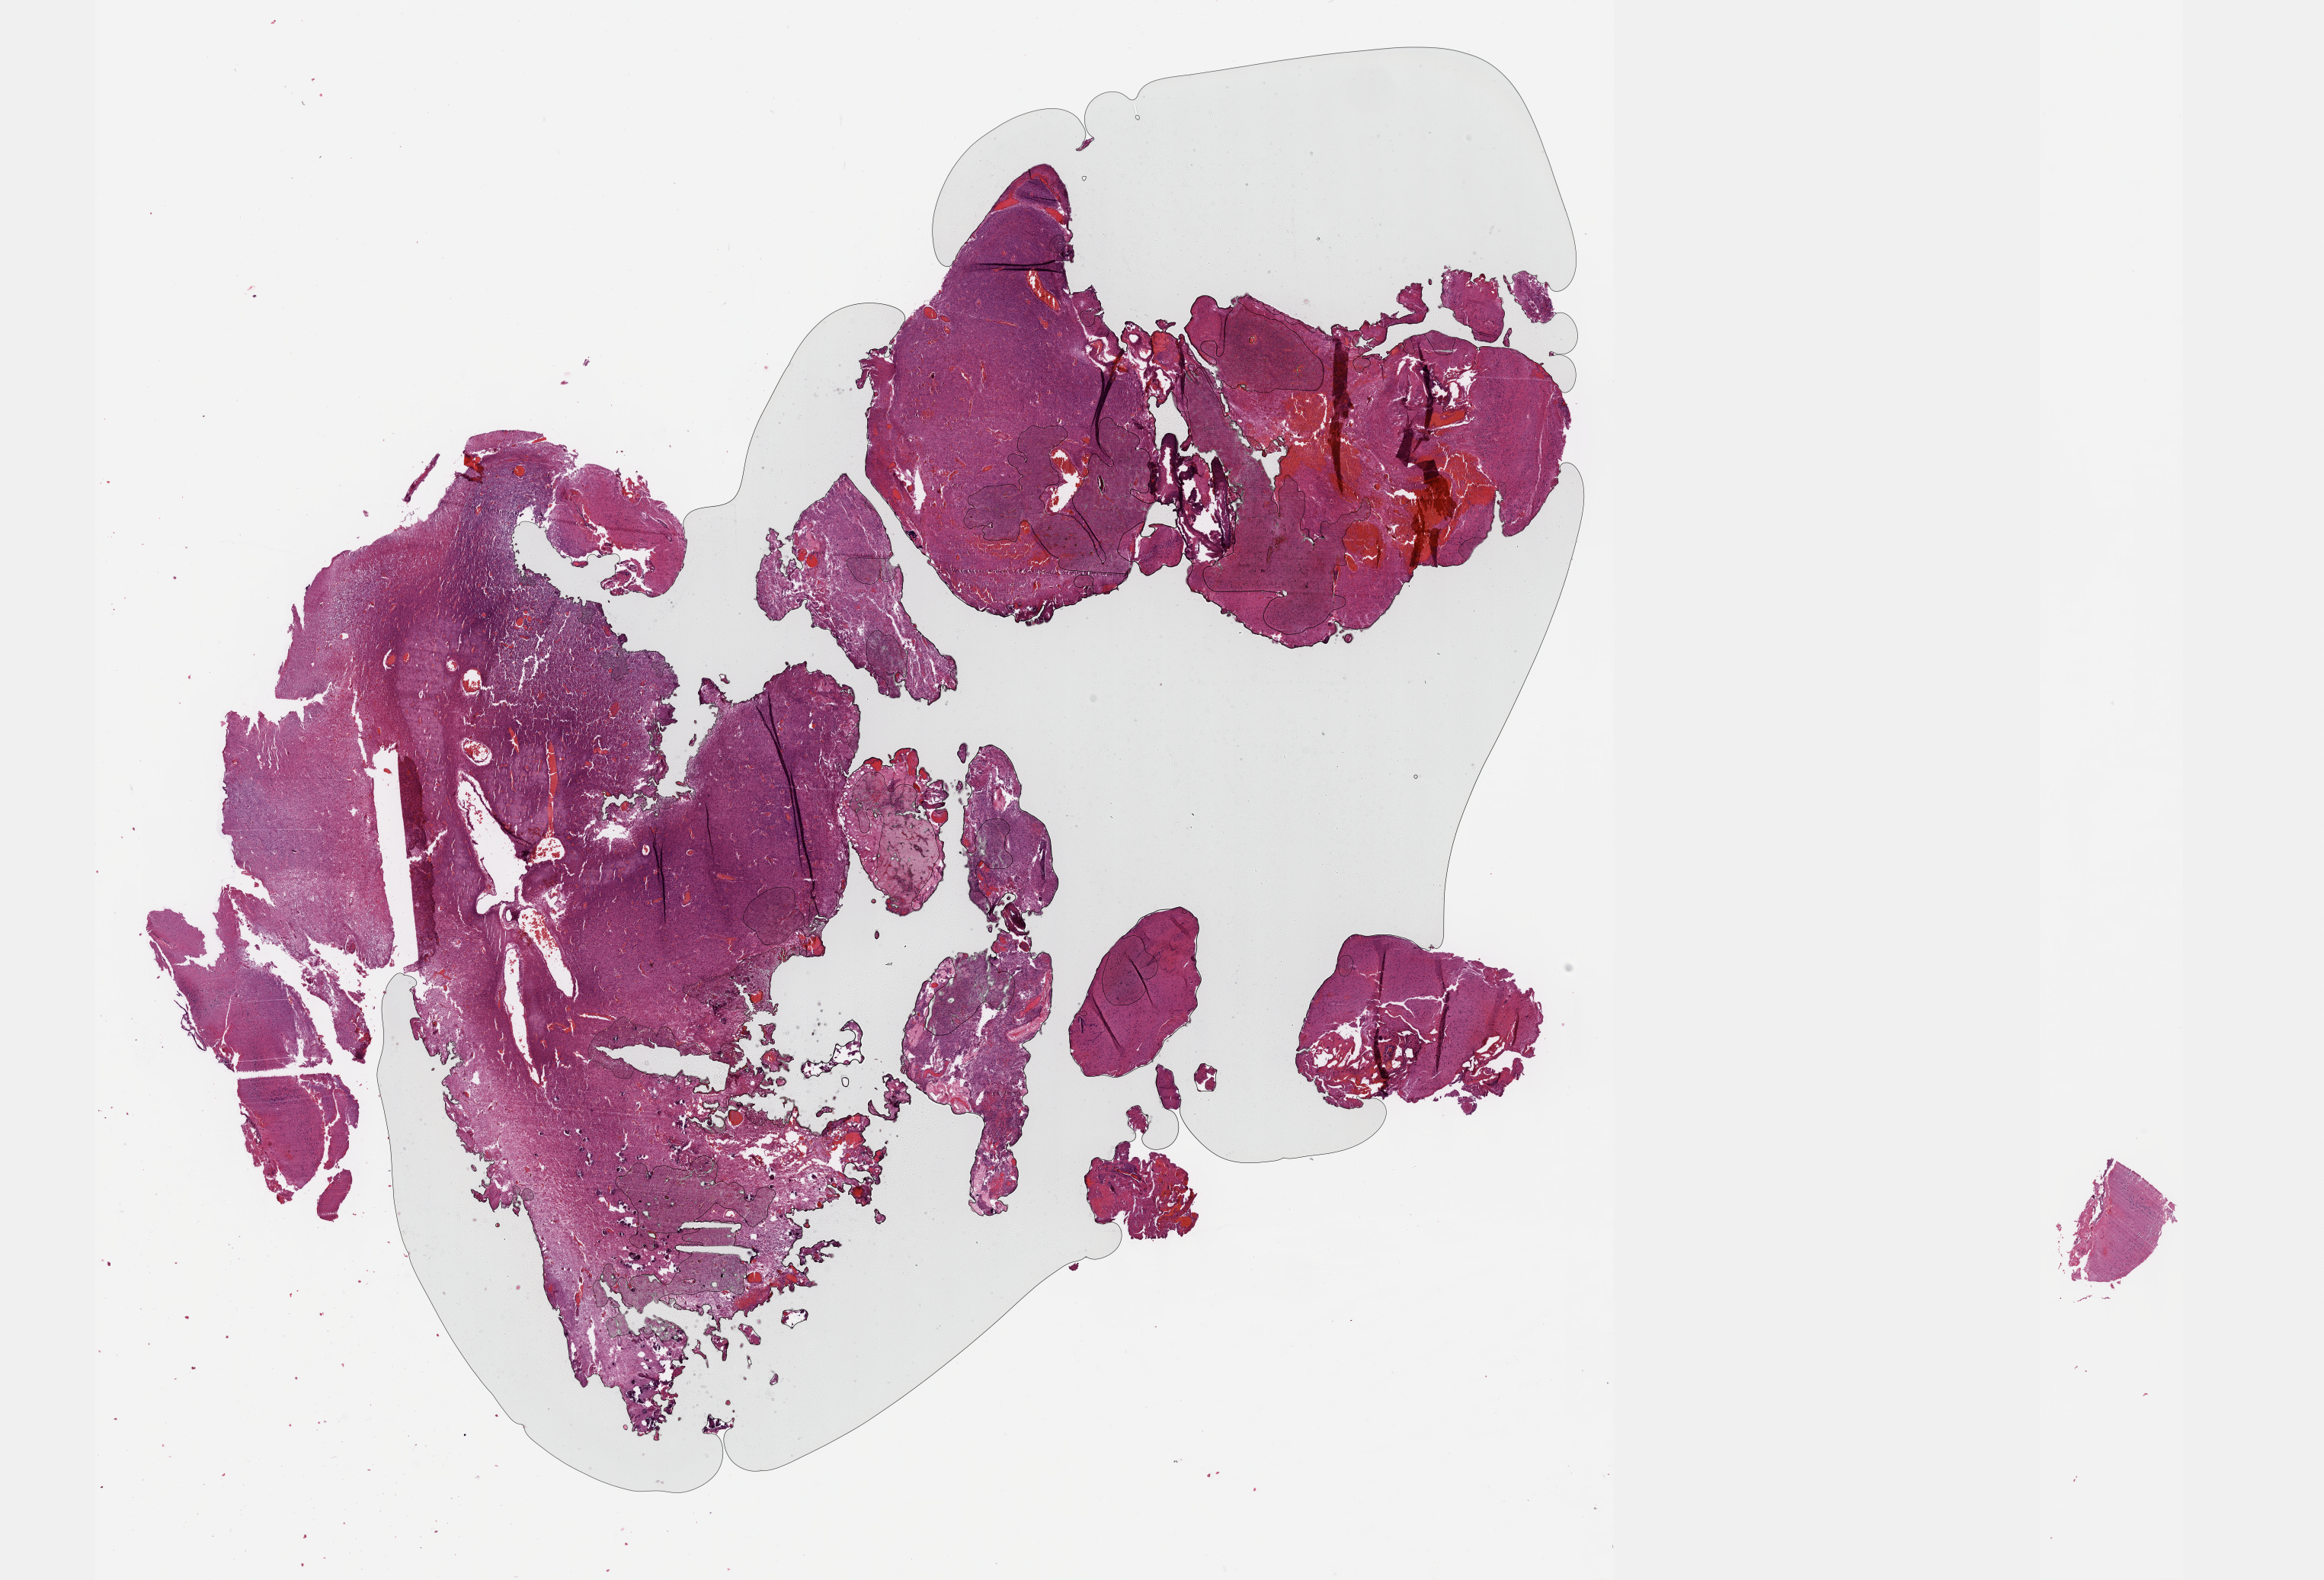
Whole-slide histology image, Hematoxylin and eosin (H&E) stained — a low-resolution overview of the entire scanned area, about 24.6 x 16.8 mm. Formalin-fixed paraffin-embedded (FFPE) diagnostic section. Sample: primary tumour, brain. Female patient; age at initial diagnosis 31 years. Histologic grade: G2 (moderately differentiated).
* diagnosis: Astrocytoma, NOS (cerebrum)